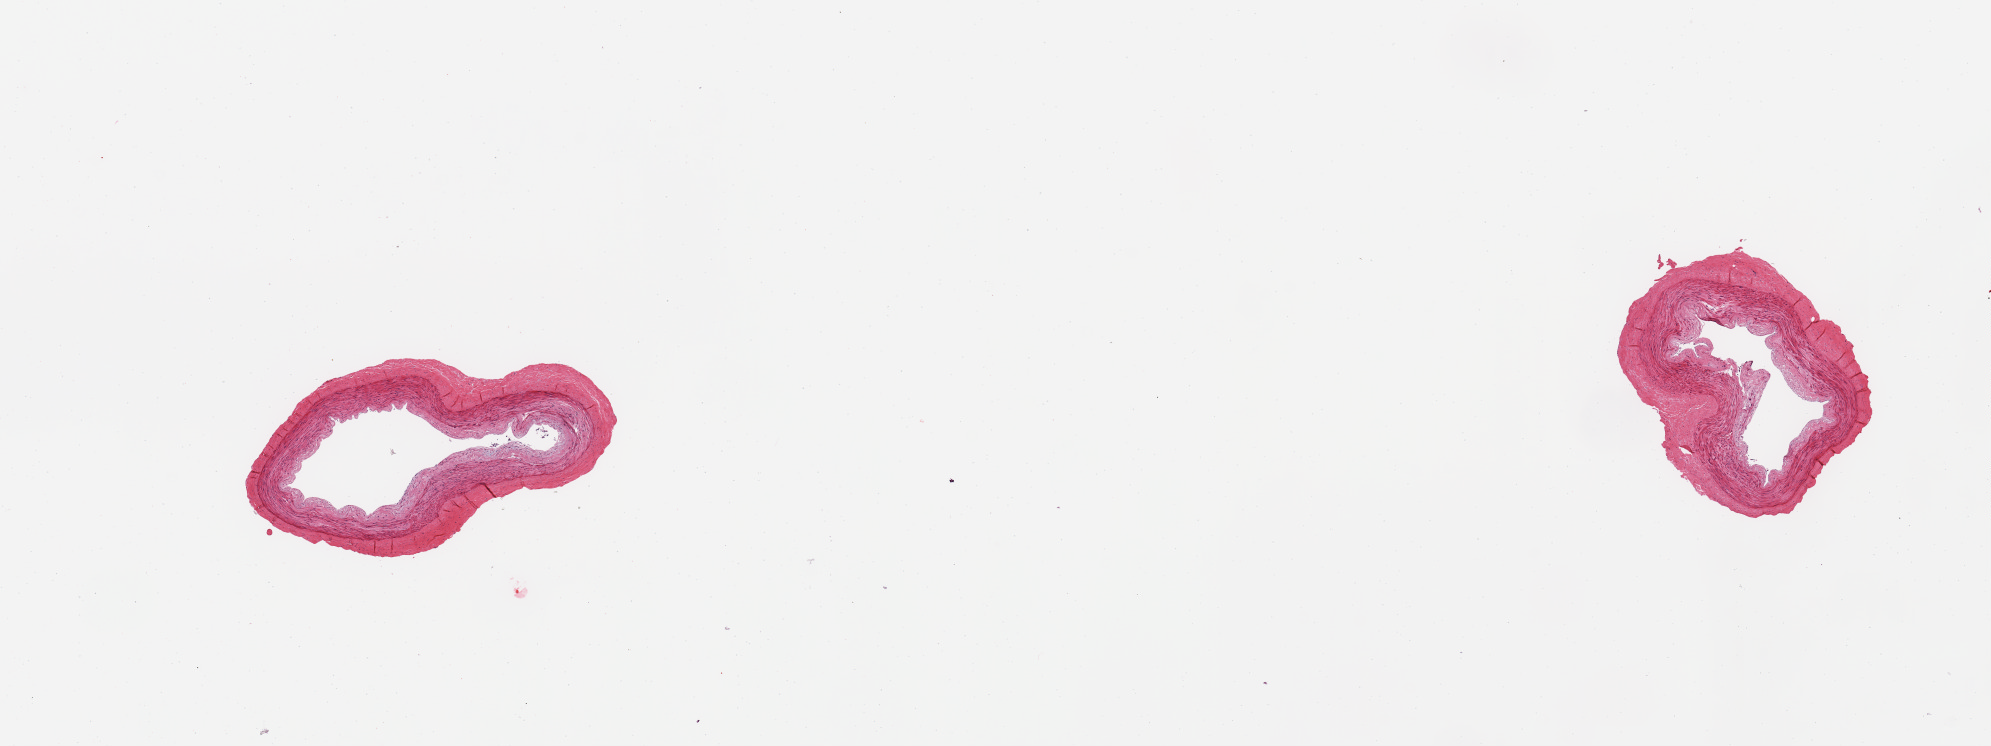
Digitized H&E-stained section, brightfield, low-resolution overview of the scanned area, about 15.8 x 5.9 mm (acquisition: 20x scan). PAXgene-fixed paraffin-embedded (PFPE) section. Target tissue: tibial artery. Tissue donor sample. Donor sex: female.
• pathologist's review note for this sample: 2 pieces, no significant atherosis or adherent fat